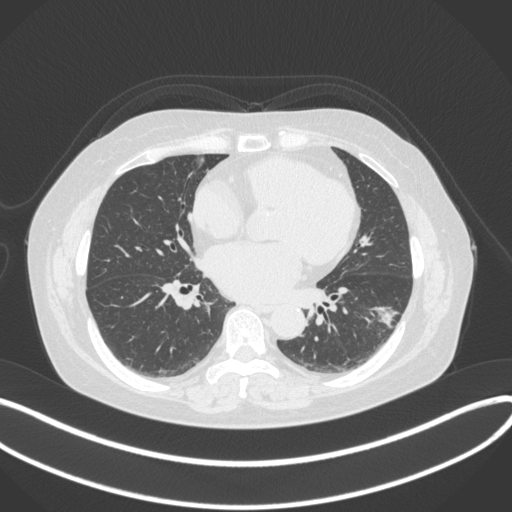
Chest CT, one axial slice. Lung window (W 1500 / L -600 HU). 1 mm slice thickness. 512 × 512 image matrix. Patient: female, 67 years. Case-level facts recorded for this patient, not image findings: clinical TNM (as recorded): T1c N0 M0.
Structures marked on this image (bounding box drawn by a radiologist):
- lung tumour (recorded histology: adenocarcinoma): bounding box <361,297,404,331> (left, top, right, bottom; pixels)